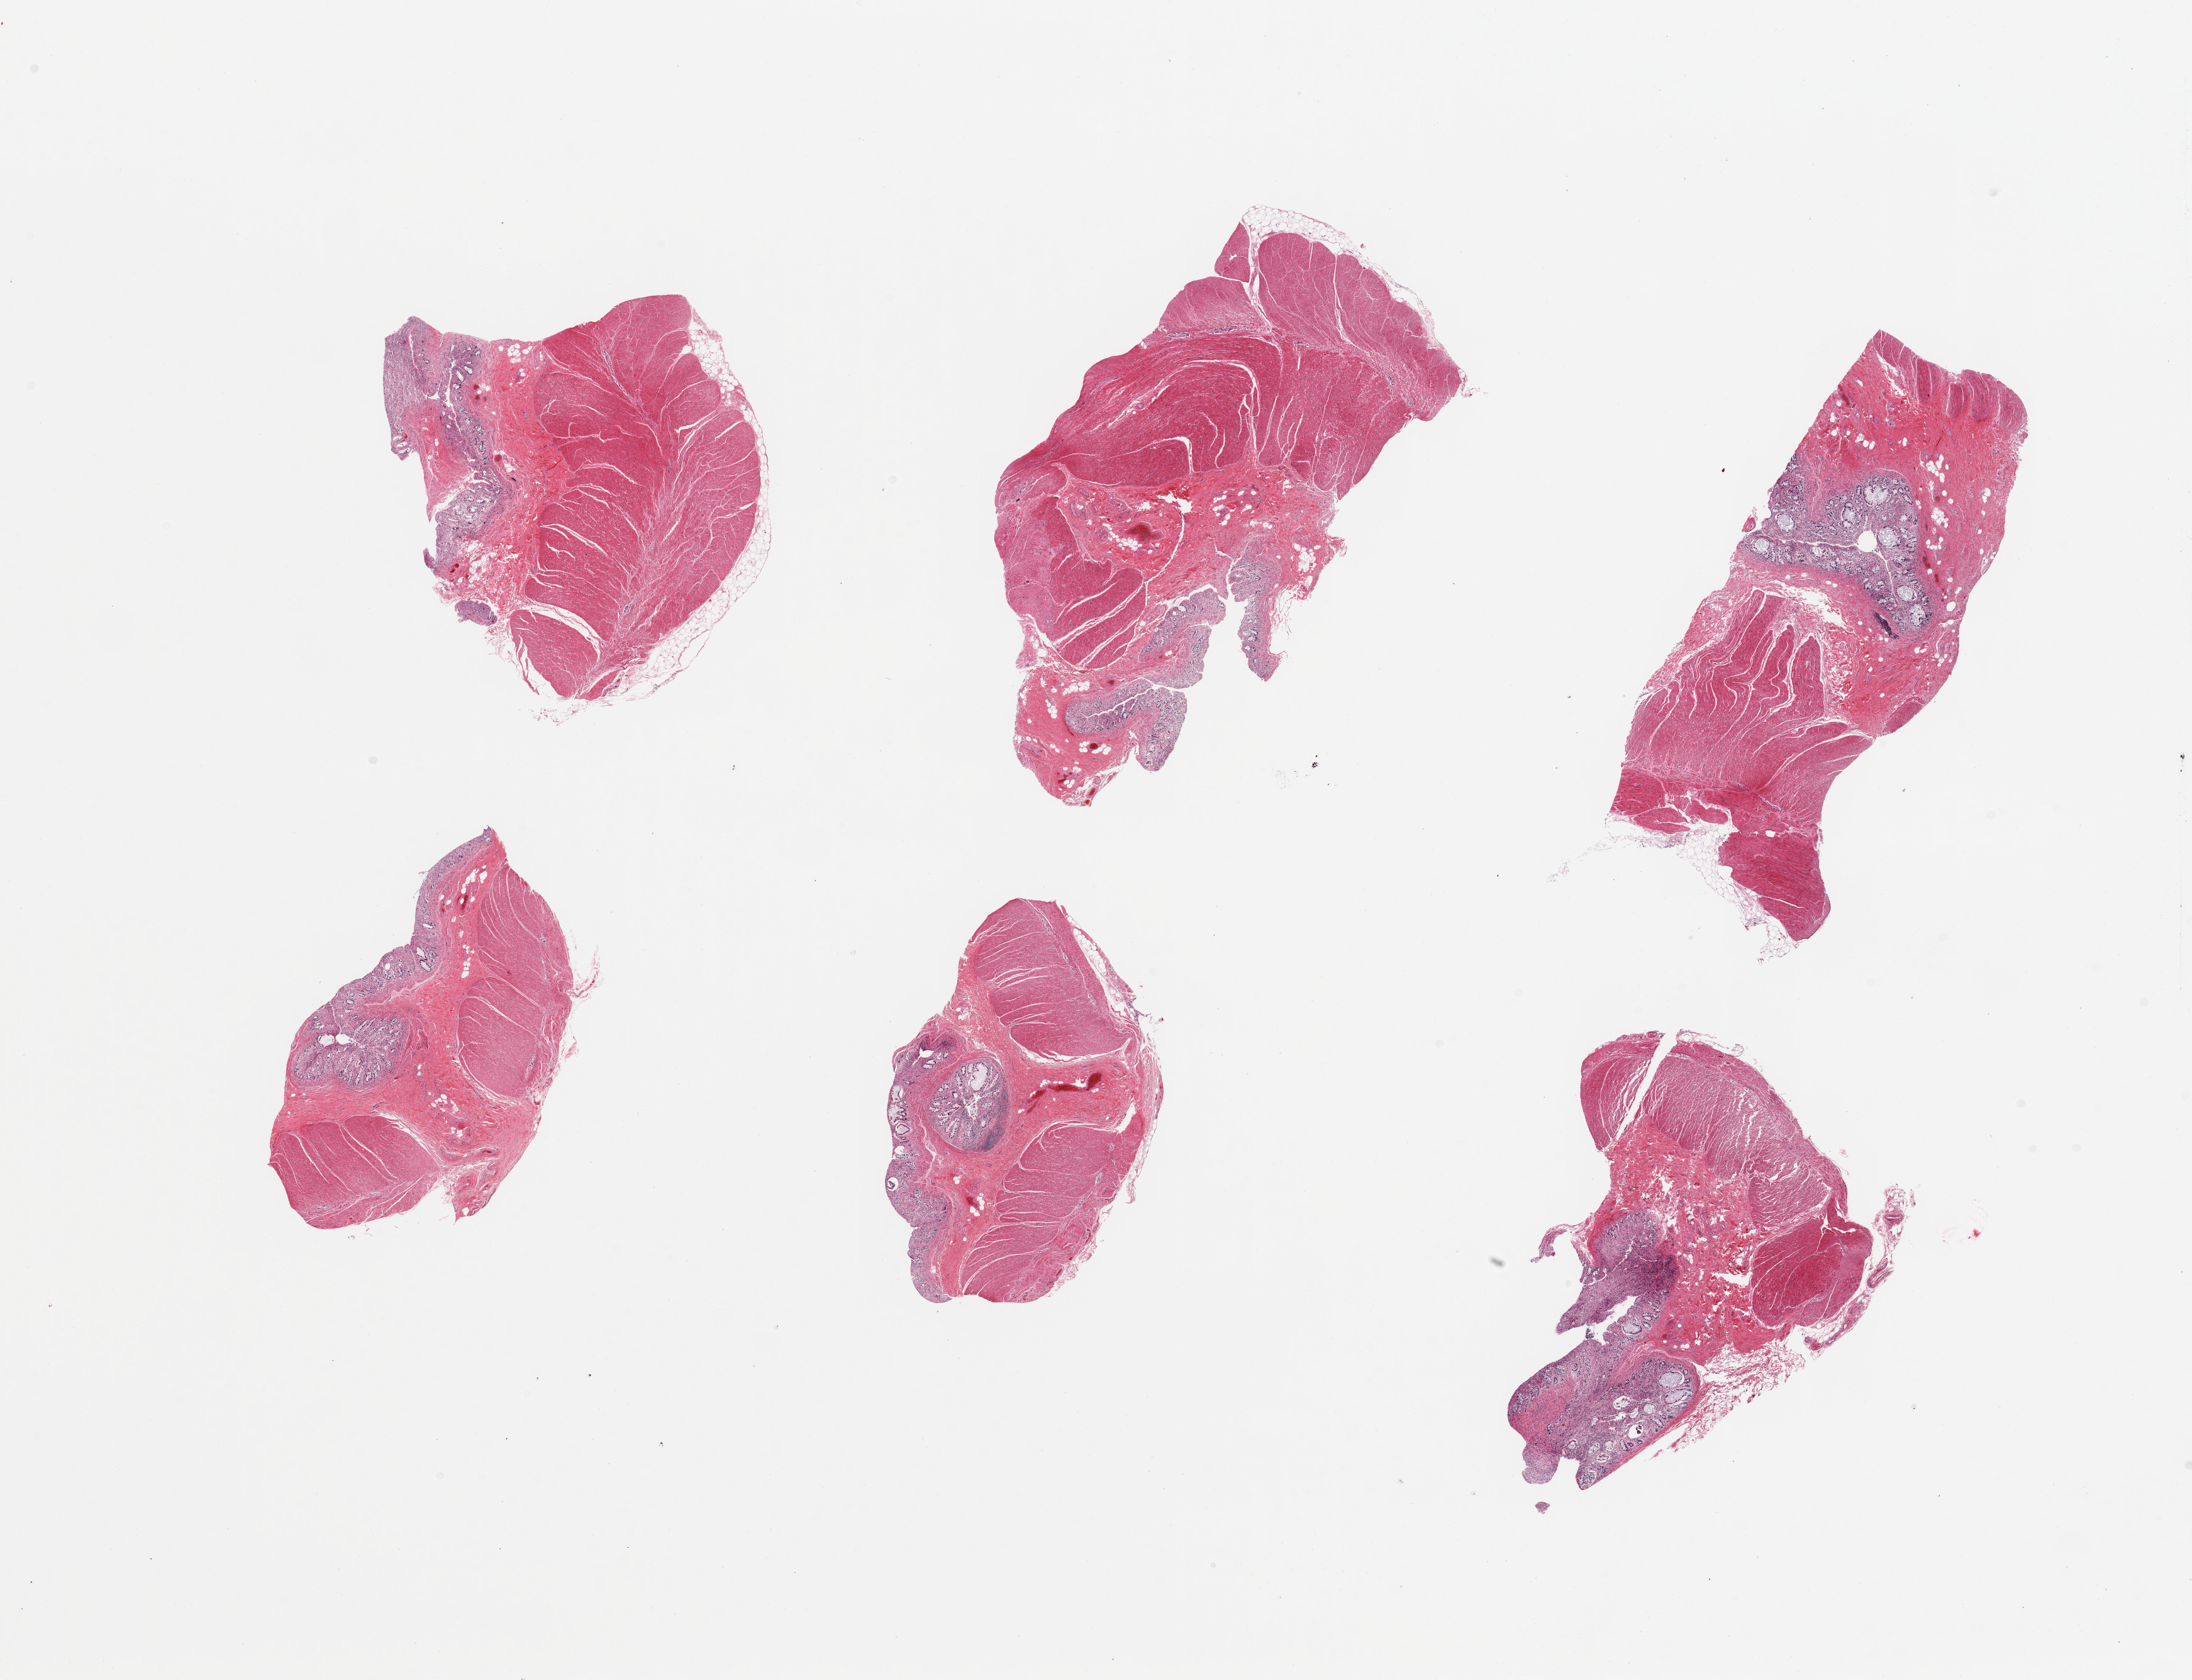
Digitized haematoxylin and eosin-stained section, a low-resolution overview of the entire scanned area, about 27.6 x 21.1 mm, PAXgene-fixed paraffin-embedded (PFPE) section, section of sigmoid colon (target tissue), donor tissue sample.
Review note (as recorded): 6 pieces, muscularis and autolyzing mucosa, intramural diverticuli present.